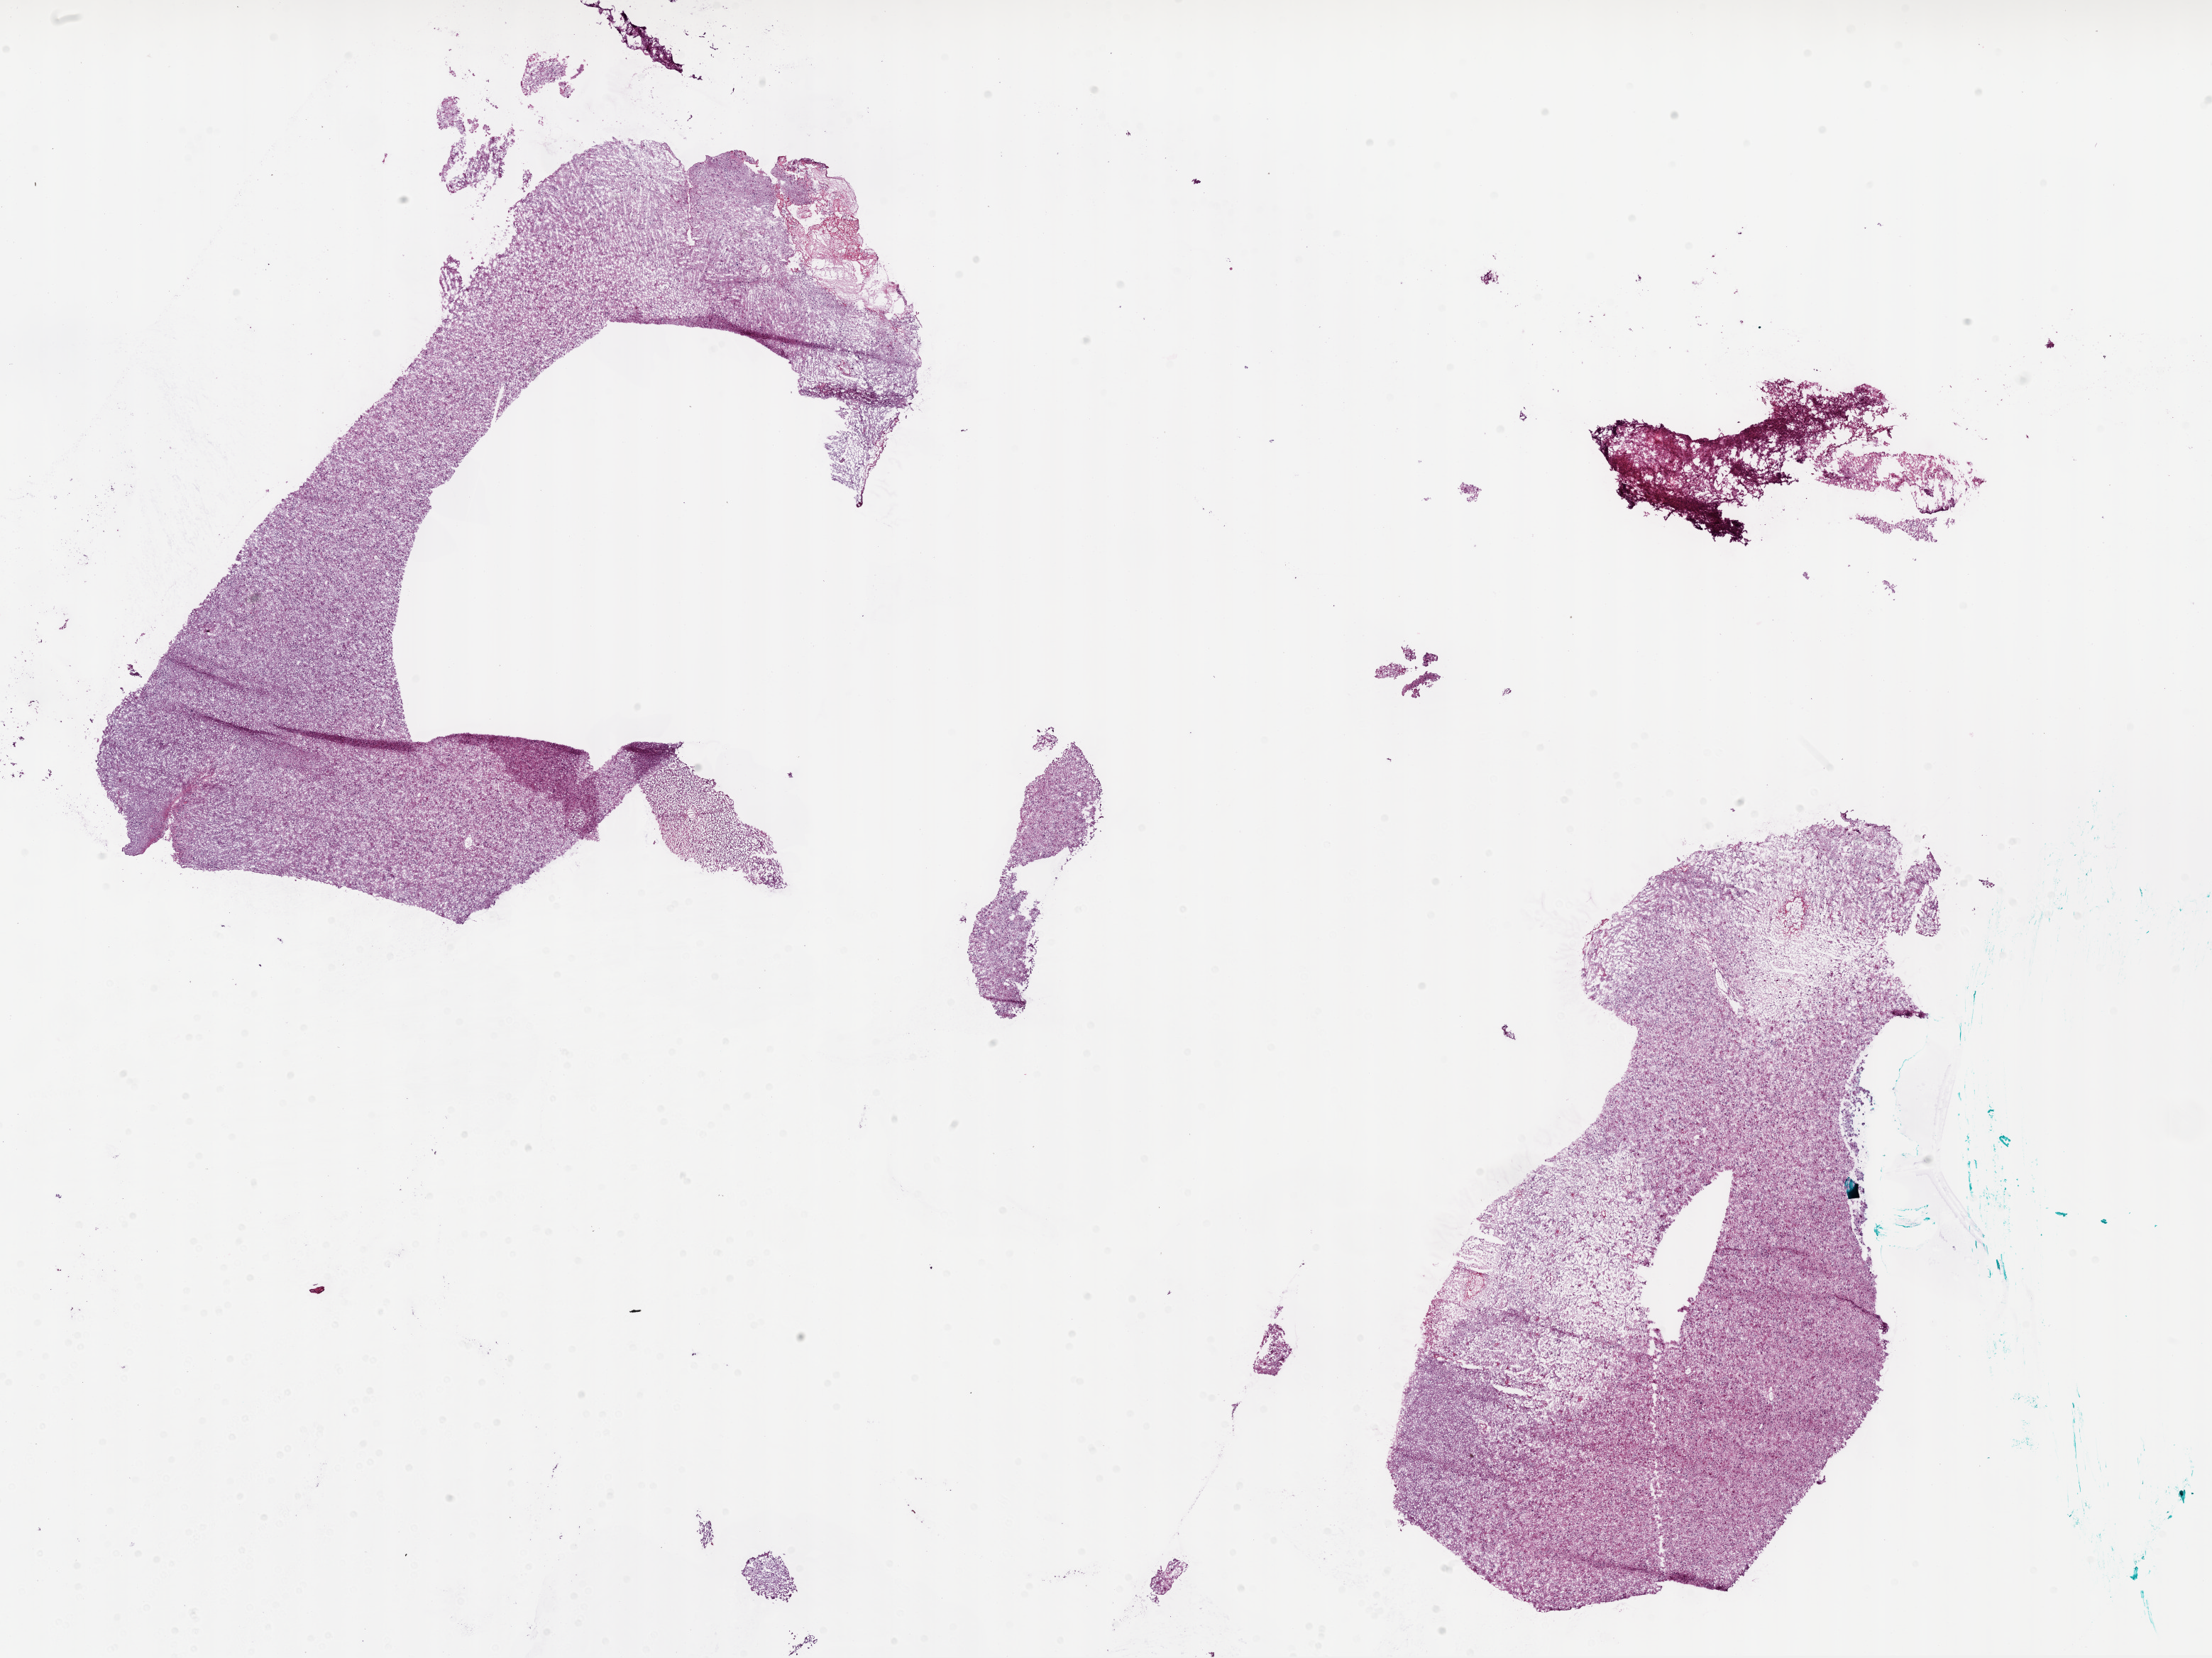
H&E whole-slide image, a low-resolution overview of the entire scanned area, about 25.1 x 18.9 mm. Frozen section. Brain, primary tumour sample. Male patient; age at initial diagnosis 85 years. Composition of this section per pathologist review: tumour cells 80%, tumour nuclei 85%, normal cells 10%, stromal cells 5%, necrosis 5%.
Diagnosis: Glioblastoma.